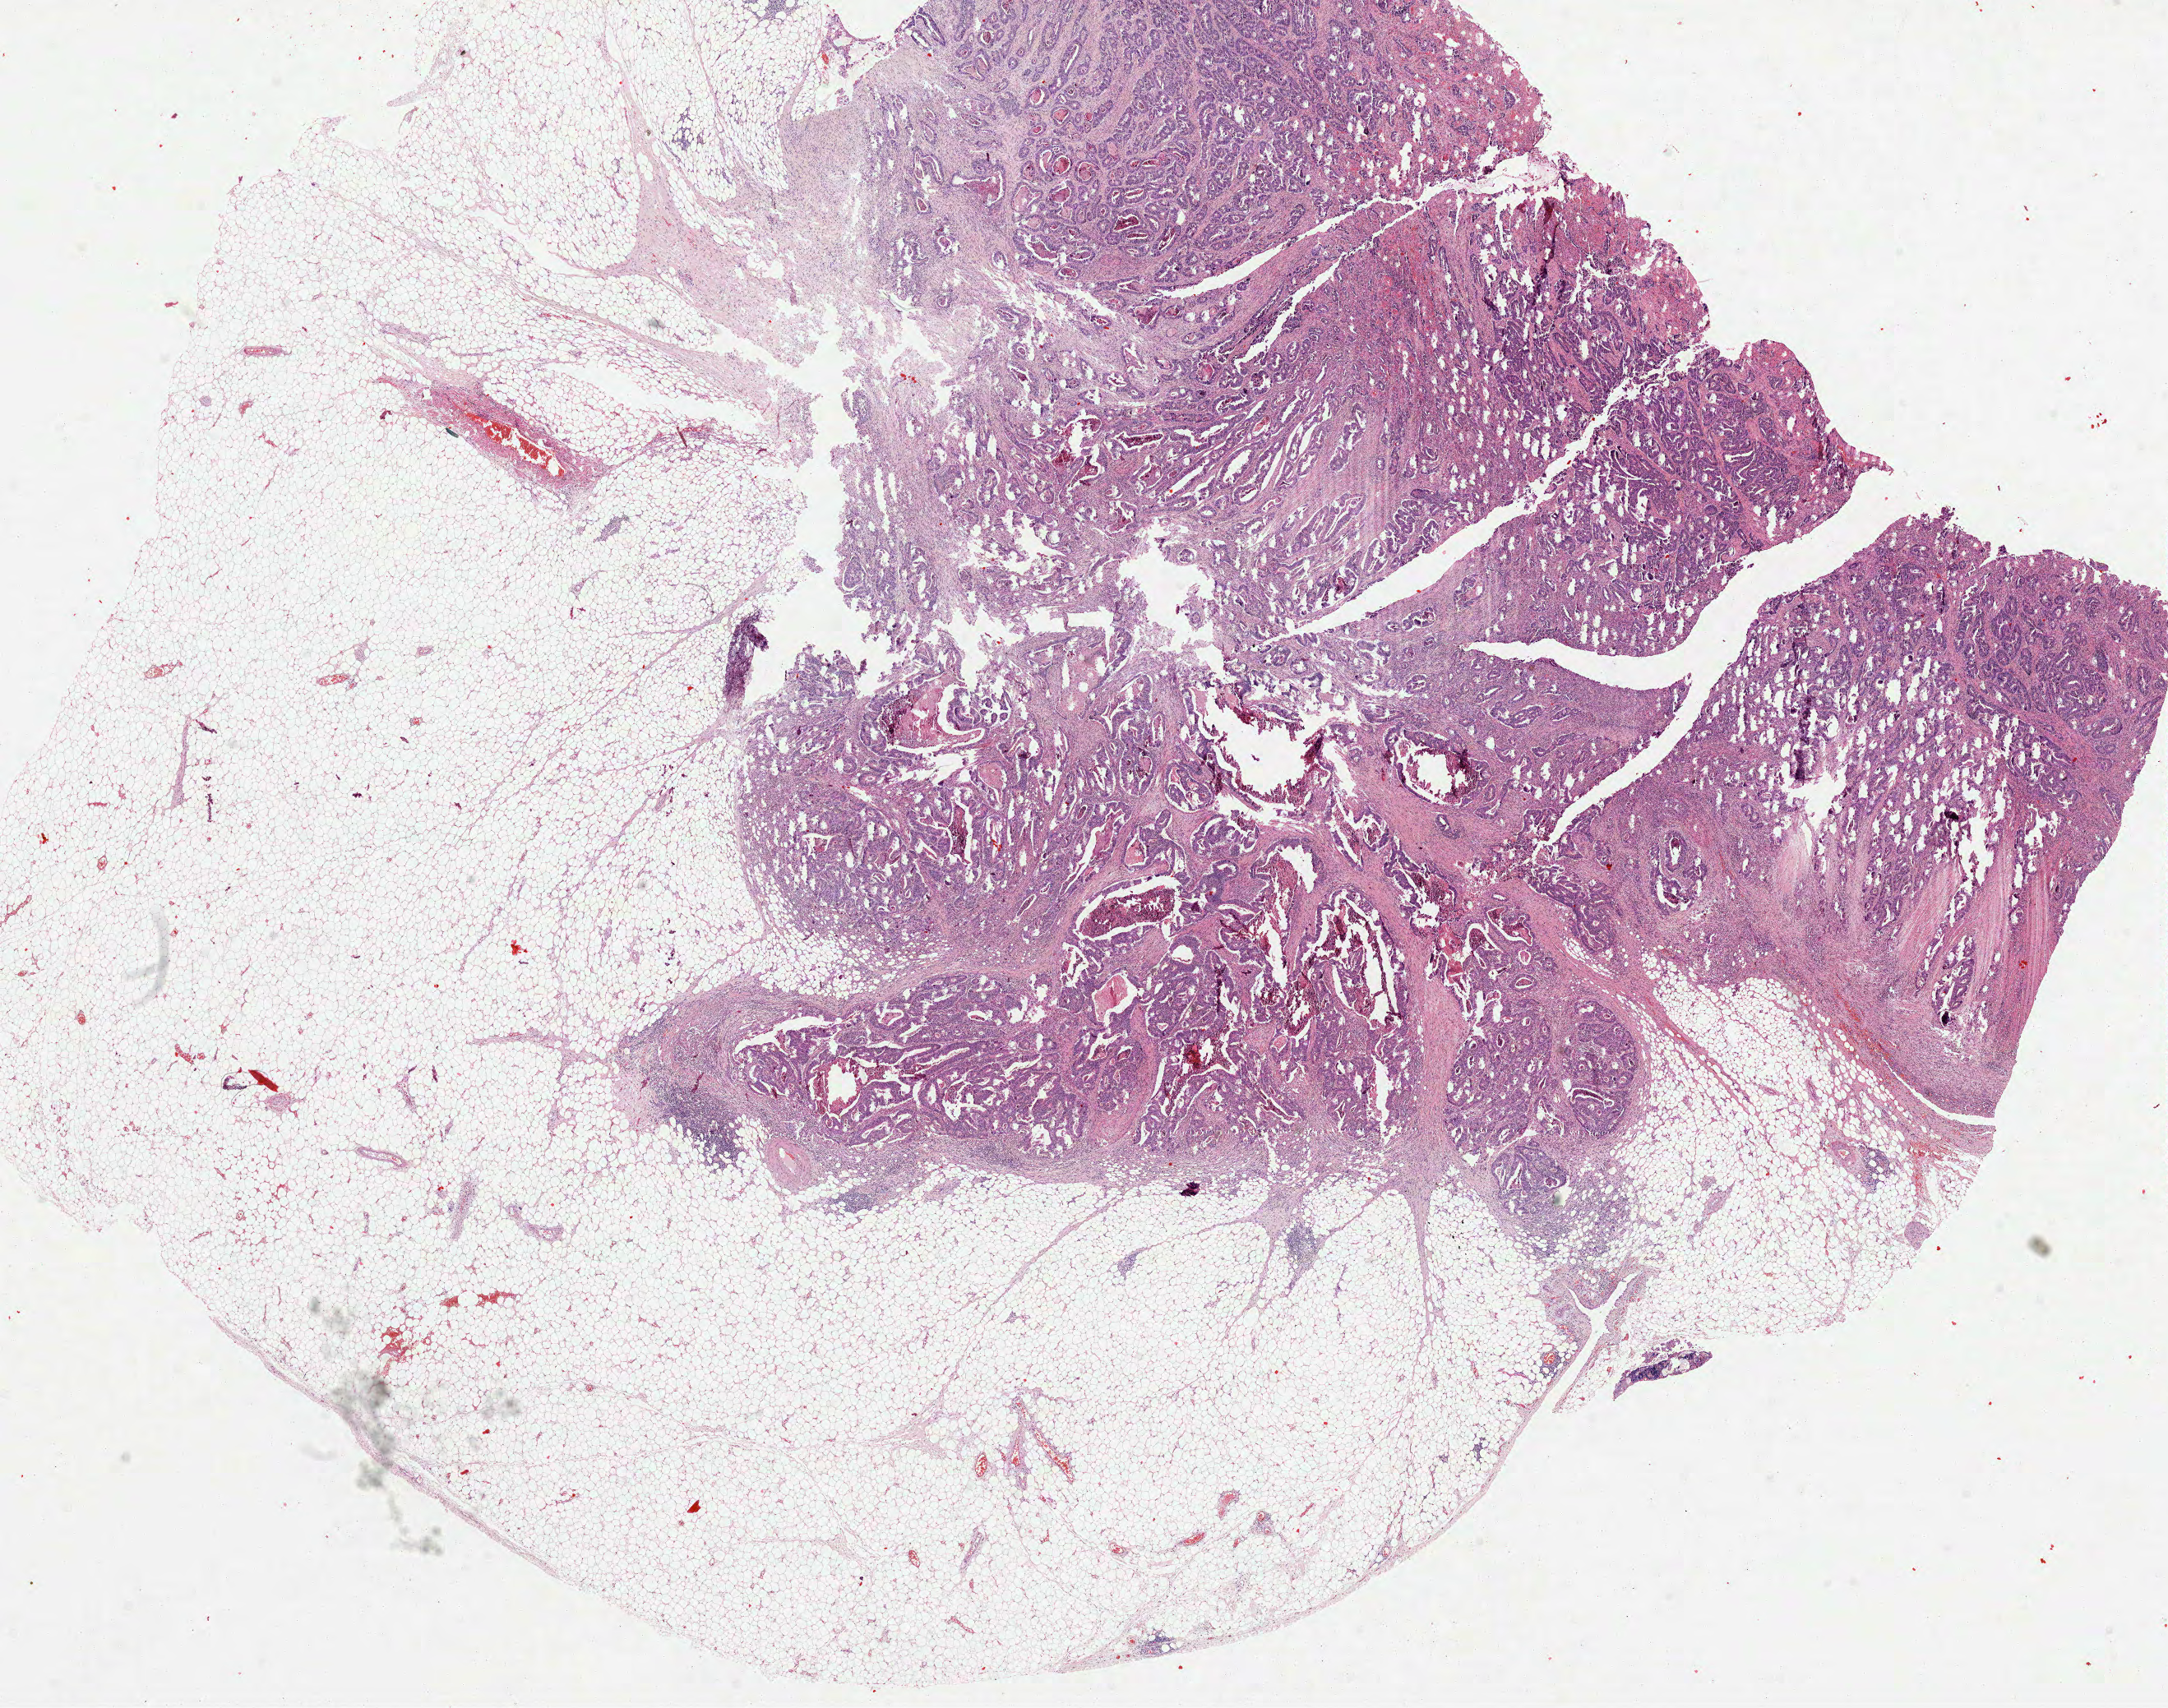
Digitized H&E-stained tissue section (whole slide), a low-resolution overview of the entire scanned area, about 21.3 x 16.8 mm (slide scanned at 40x); formalin-fixed paraffin-embedded (FFPE) diagnostic section; sample: primary tumour, rectum. Female, age 78 years at initial diagnosis.
Diagnosis: Tubular adenocarcinoma. Lymph nodes positive (case pathology): 0 of 19 examined. AJCC pathologic stage: IIA (7th edition).